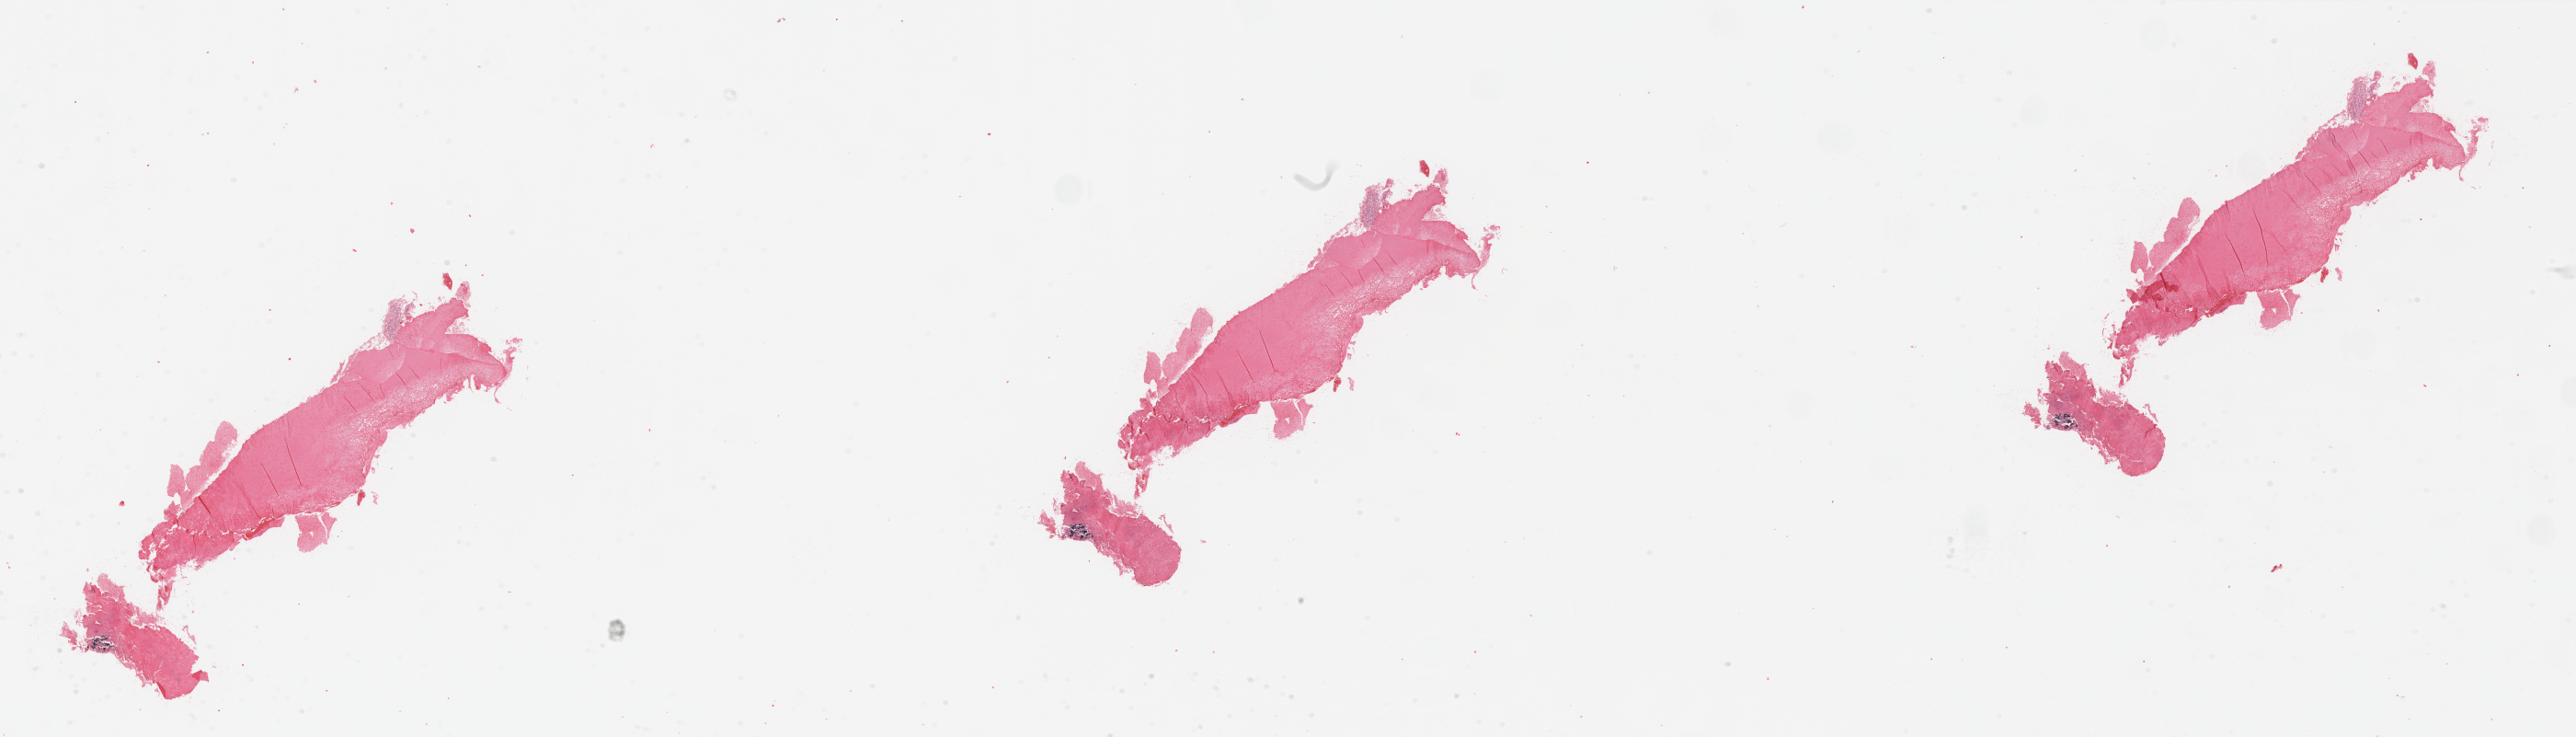
Whole-slide histology image, H&E, whole scanned area (about 44.3 x 12.7 mm, from a 20x scan) shown as a low-resolution overview. Tumour tissue sample, kidney. Patient: female, age 51 years. Histologic grade: G3 (poorly differentiated).
• AJCC pathologic stage: IV
• histologic diagnosis: Renal cell carcinoma, NOS